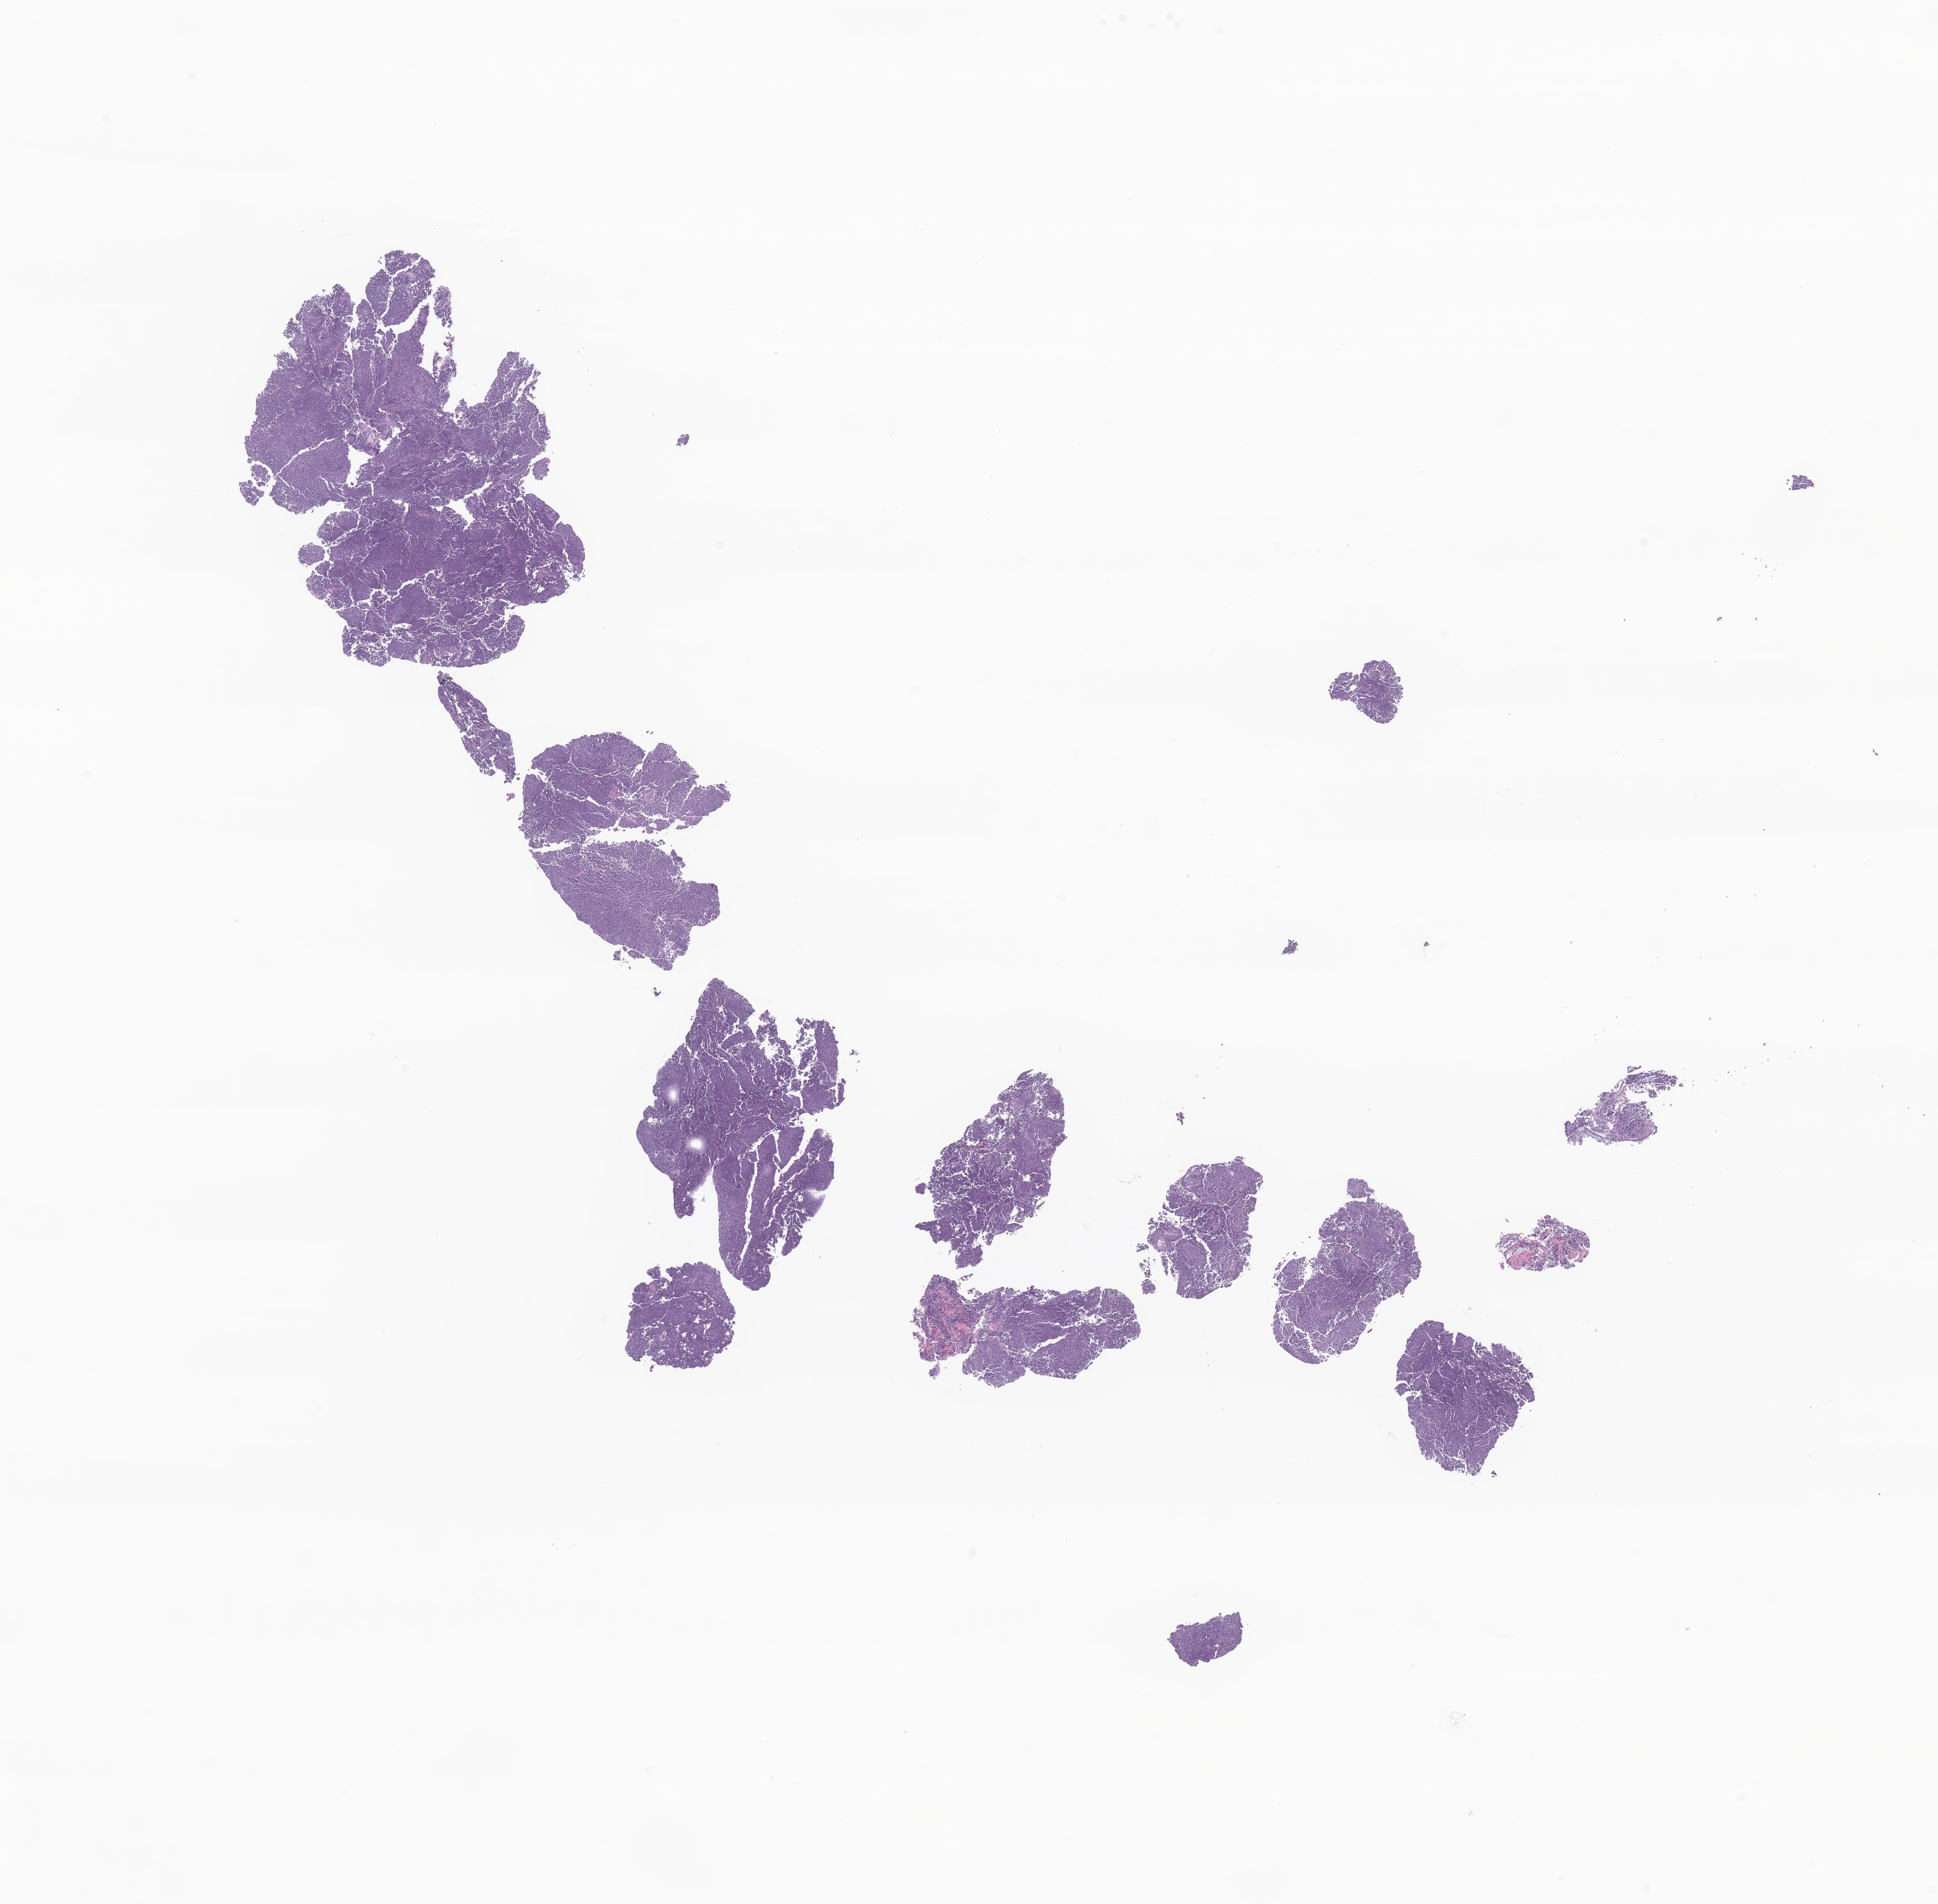
Digitized haematoxylin and eosin-stained section of tumor tissue from the pelvis — whole scanned area (about 15.5 x 15.2 mm) shown as a low-resolution overview, formalin-fixed, paraffin-embedded (FFPE) tissue. Patient male; age 649 days.
Recorded diagnosis: Sarcoma, NOS.